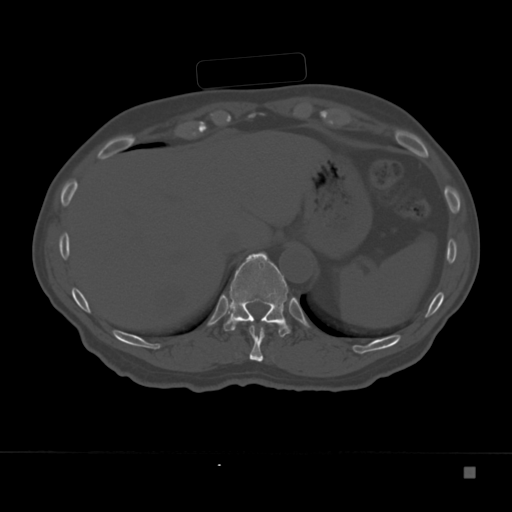
CT including the spine, one axial slice. Slice 160 of 332 in the series (ordered by position). Reconstruction kernel Br40s. 120 kVp. Bone window (W 1800 / L 400 HU). 1.5 mm slice thickness. 512 × 512 image matrix. Patient: male, 72 years. Case-level facts recorded for this patient, not image findings: primary cancer: skeletal.
Outlined on this slice (semi-automatic segmentation, software-assisted and operator-edited):
- T10 vertebra: box from (x=242, y=321) to (x=283, y=362) px
- T11 vertebra: (x=224, y=252)–(x=291, y=337)